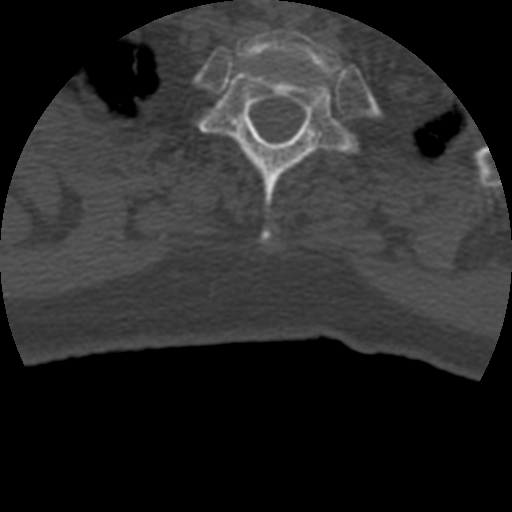
CT including the spine, one axial slice; position 370 of 399 along the scan axis; reconstruction kernel STANDARD; 120 kVp; bone window (W 1800 / L 400 HU); 512 × 512 image matrix. Patient age 69 years. Case-level facts recorded for this patient, not image findings: primary cancer: prostate.
Annotated regions visible in this slice (semi-automatically segmented with operator editing):
- T1 vertebra: bounding box [x1, y1, x2, y2] px = [237, 29, 340, 91]
- T2 vertebra: [200, 66, 355, 245]